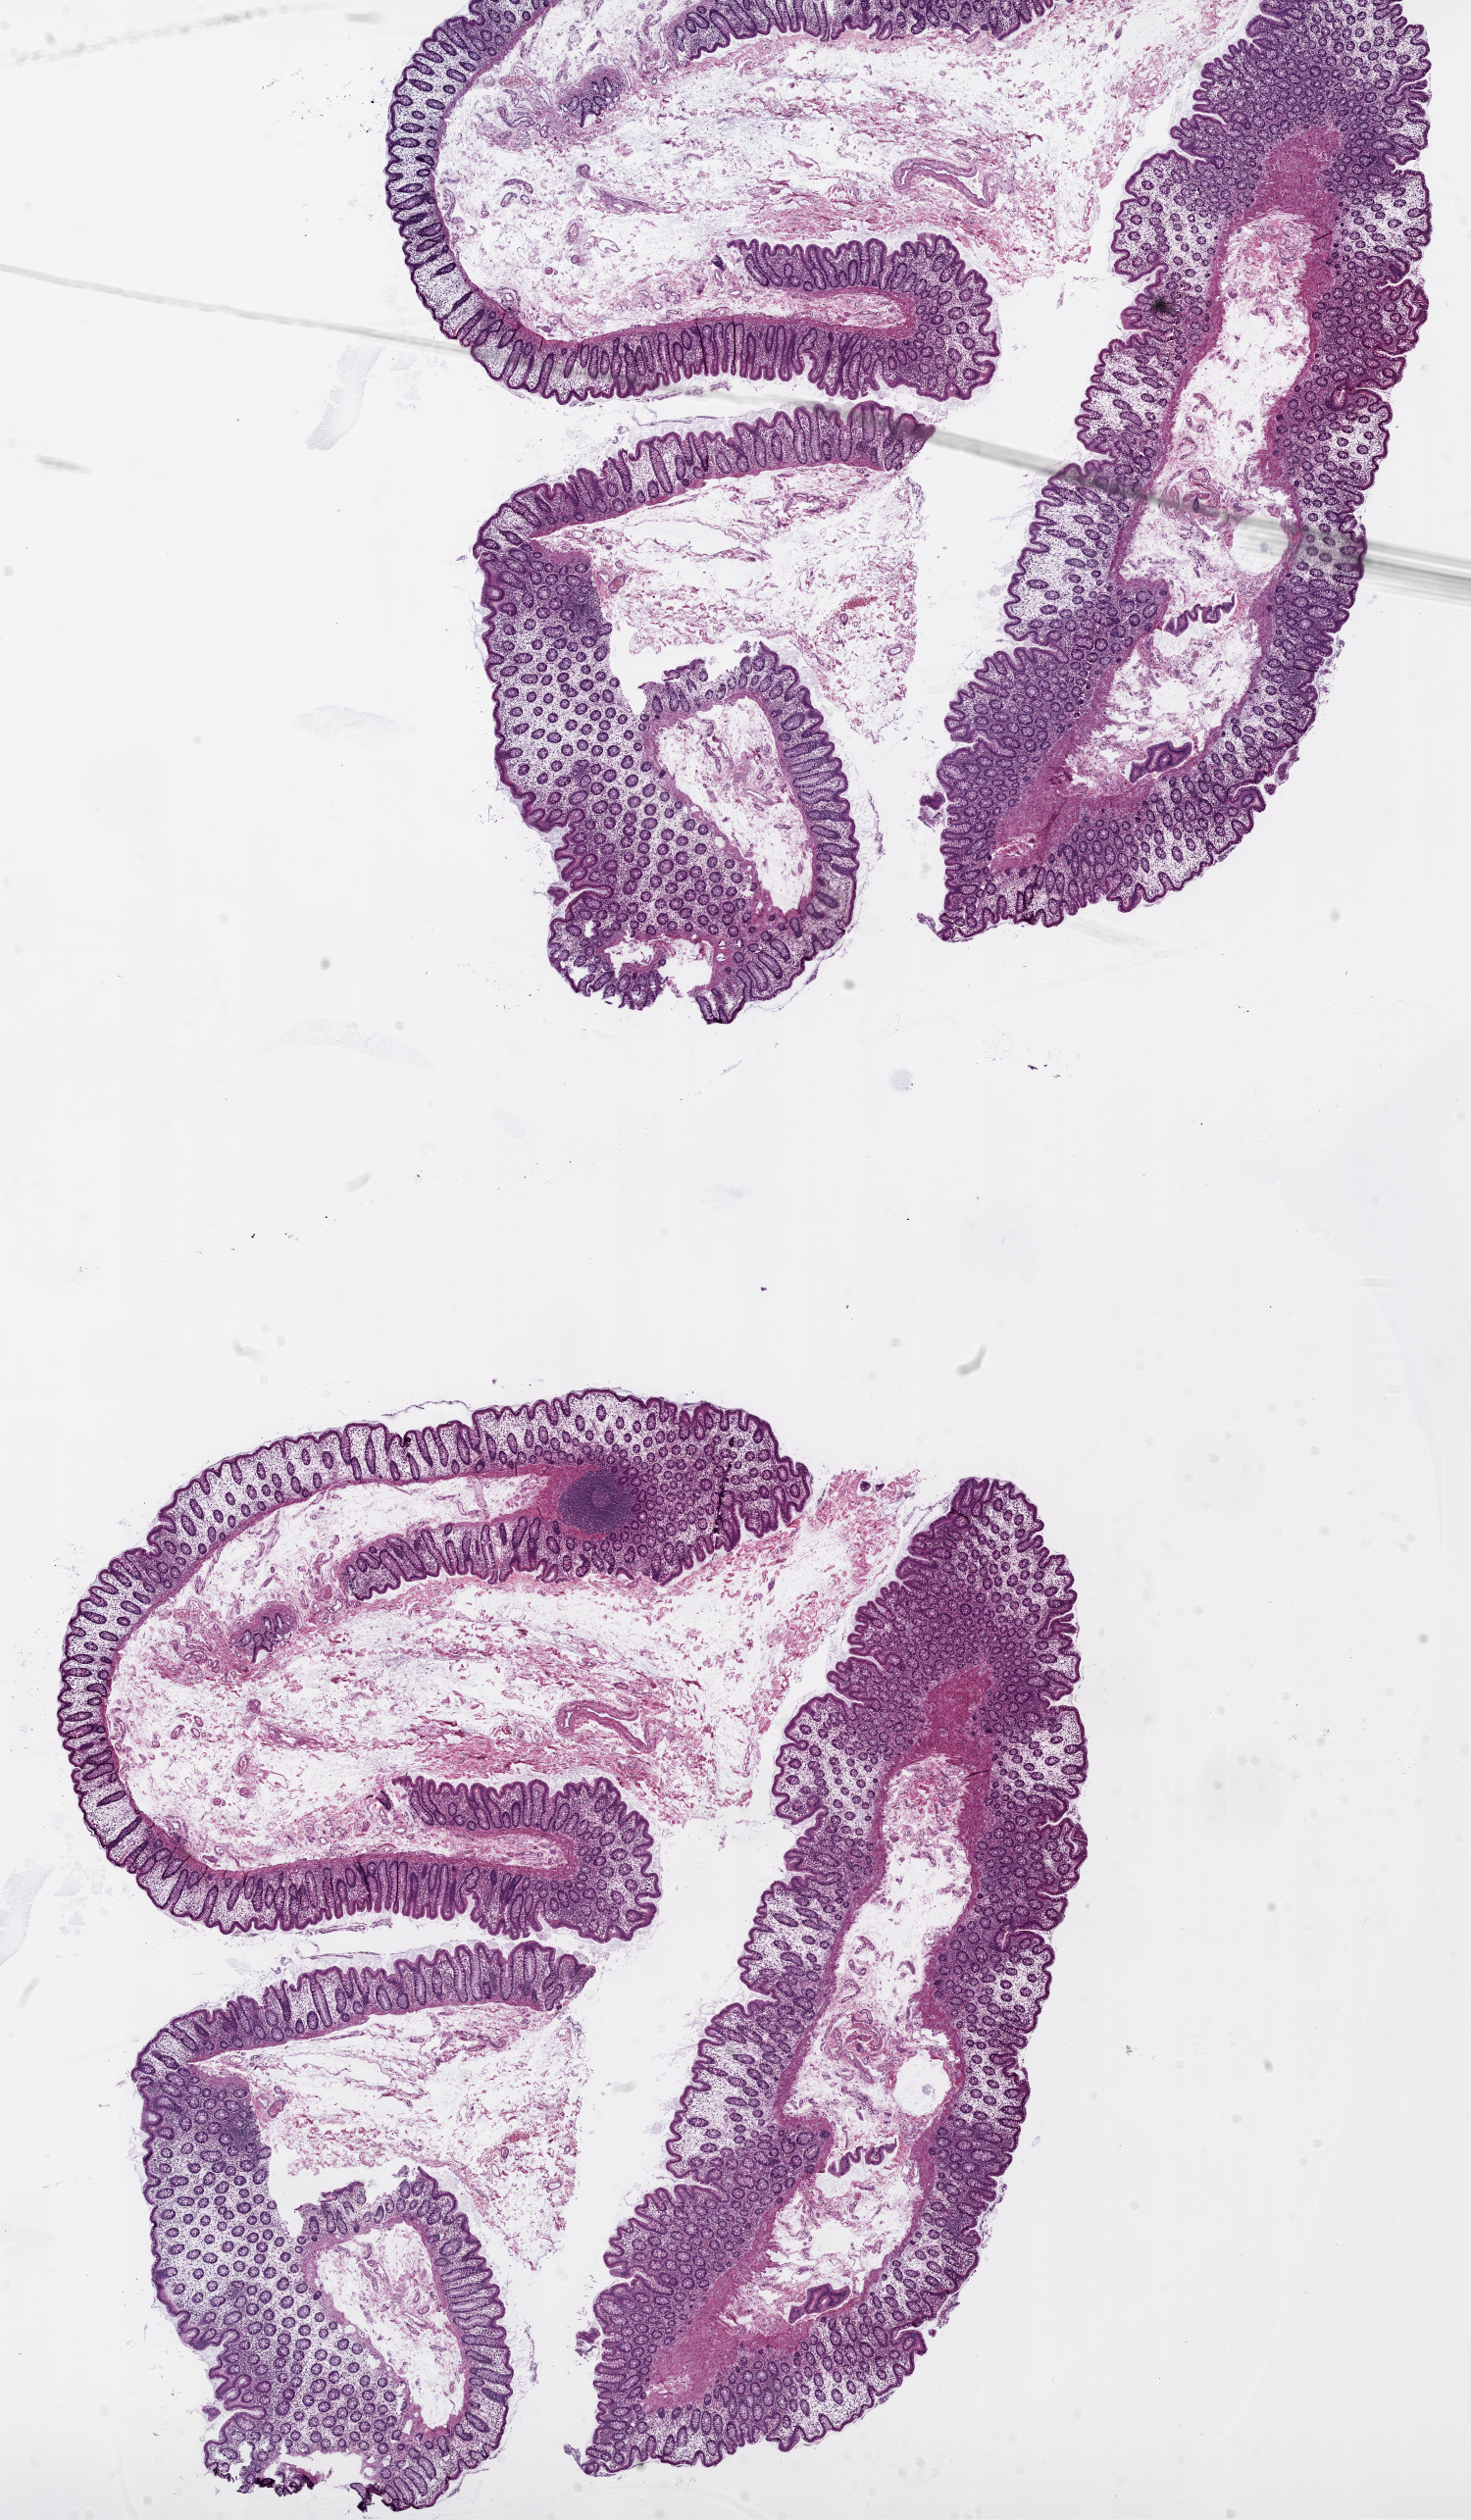
Whole-slide histology image, H&E, low-resolution overview of the scanned area, about 12.0 x 20.6 mm (from a 20x scan); frozen section; colon, solid tissue normal (non-tumour tissue) sample. Female patient; age at initial diagnosis 71 years.
* this section: solid tissue normal (non-tumour) sample from the same patient
* patient diagnosis: Mucinous adenocarcinoma